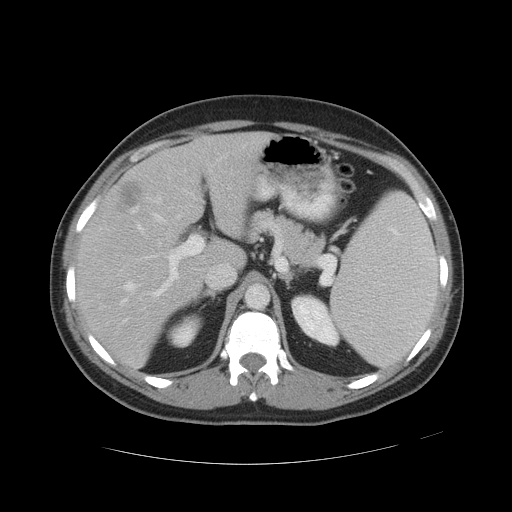
Contrast-enhanced abdominal CT, one axial slice. Position 32 of 49 along the scan axis. Reconstruction kernel STANDARD. Soft-tissue window (W 400 / L 40 HU). 5 mm slice thickness. 512 × 512 image matrix. Male patient, age 42 years. Case-level facts recorded for this patient, not image findings: diagnosis: colorectal cancer liver metastases, imaged before liver resection; multiple liver metastases: yes; largest metastasis: 2.8 cm; disease in both lobes: yes.
Annotated regions visible in this slice (expert manual segmentation):
- hepatic veins: box from (x=121, y=169) to (x=212, y=304) px
- liver: (x=77, y=133)–(x=266, y=366)
- planned liver remnant (the part of the liver to remain after resection): (x=77, y=133)–(x=265, y=366)
- portal vein (with intrahepatic branches): (x=146, y=187)–(x=230, y=297)
- liver metastasis: (x=118, y=186)–(x=141, y=212)